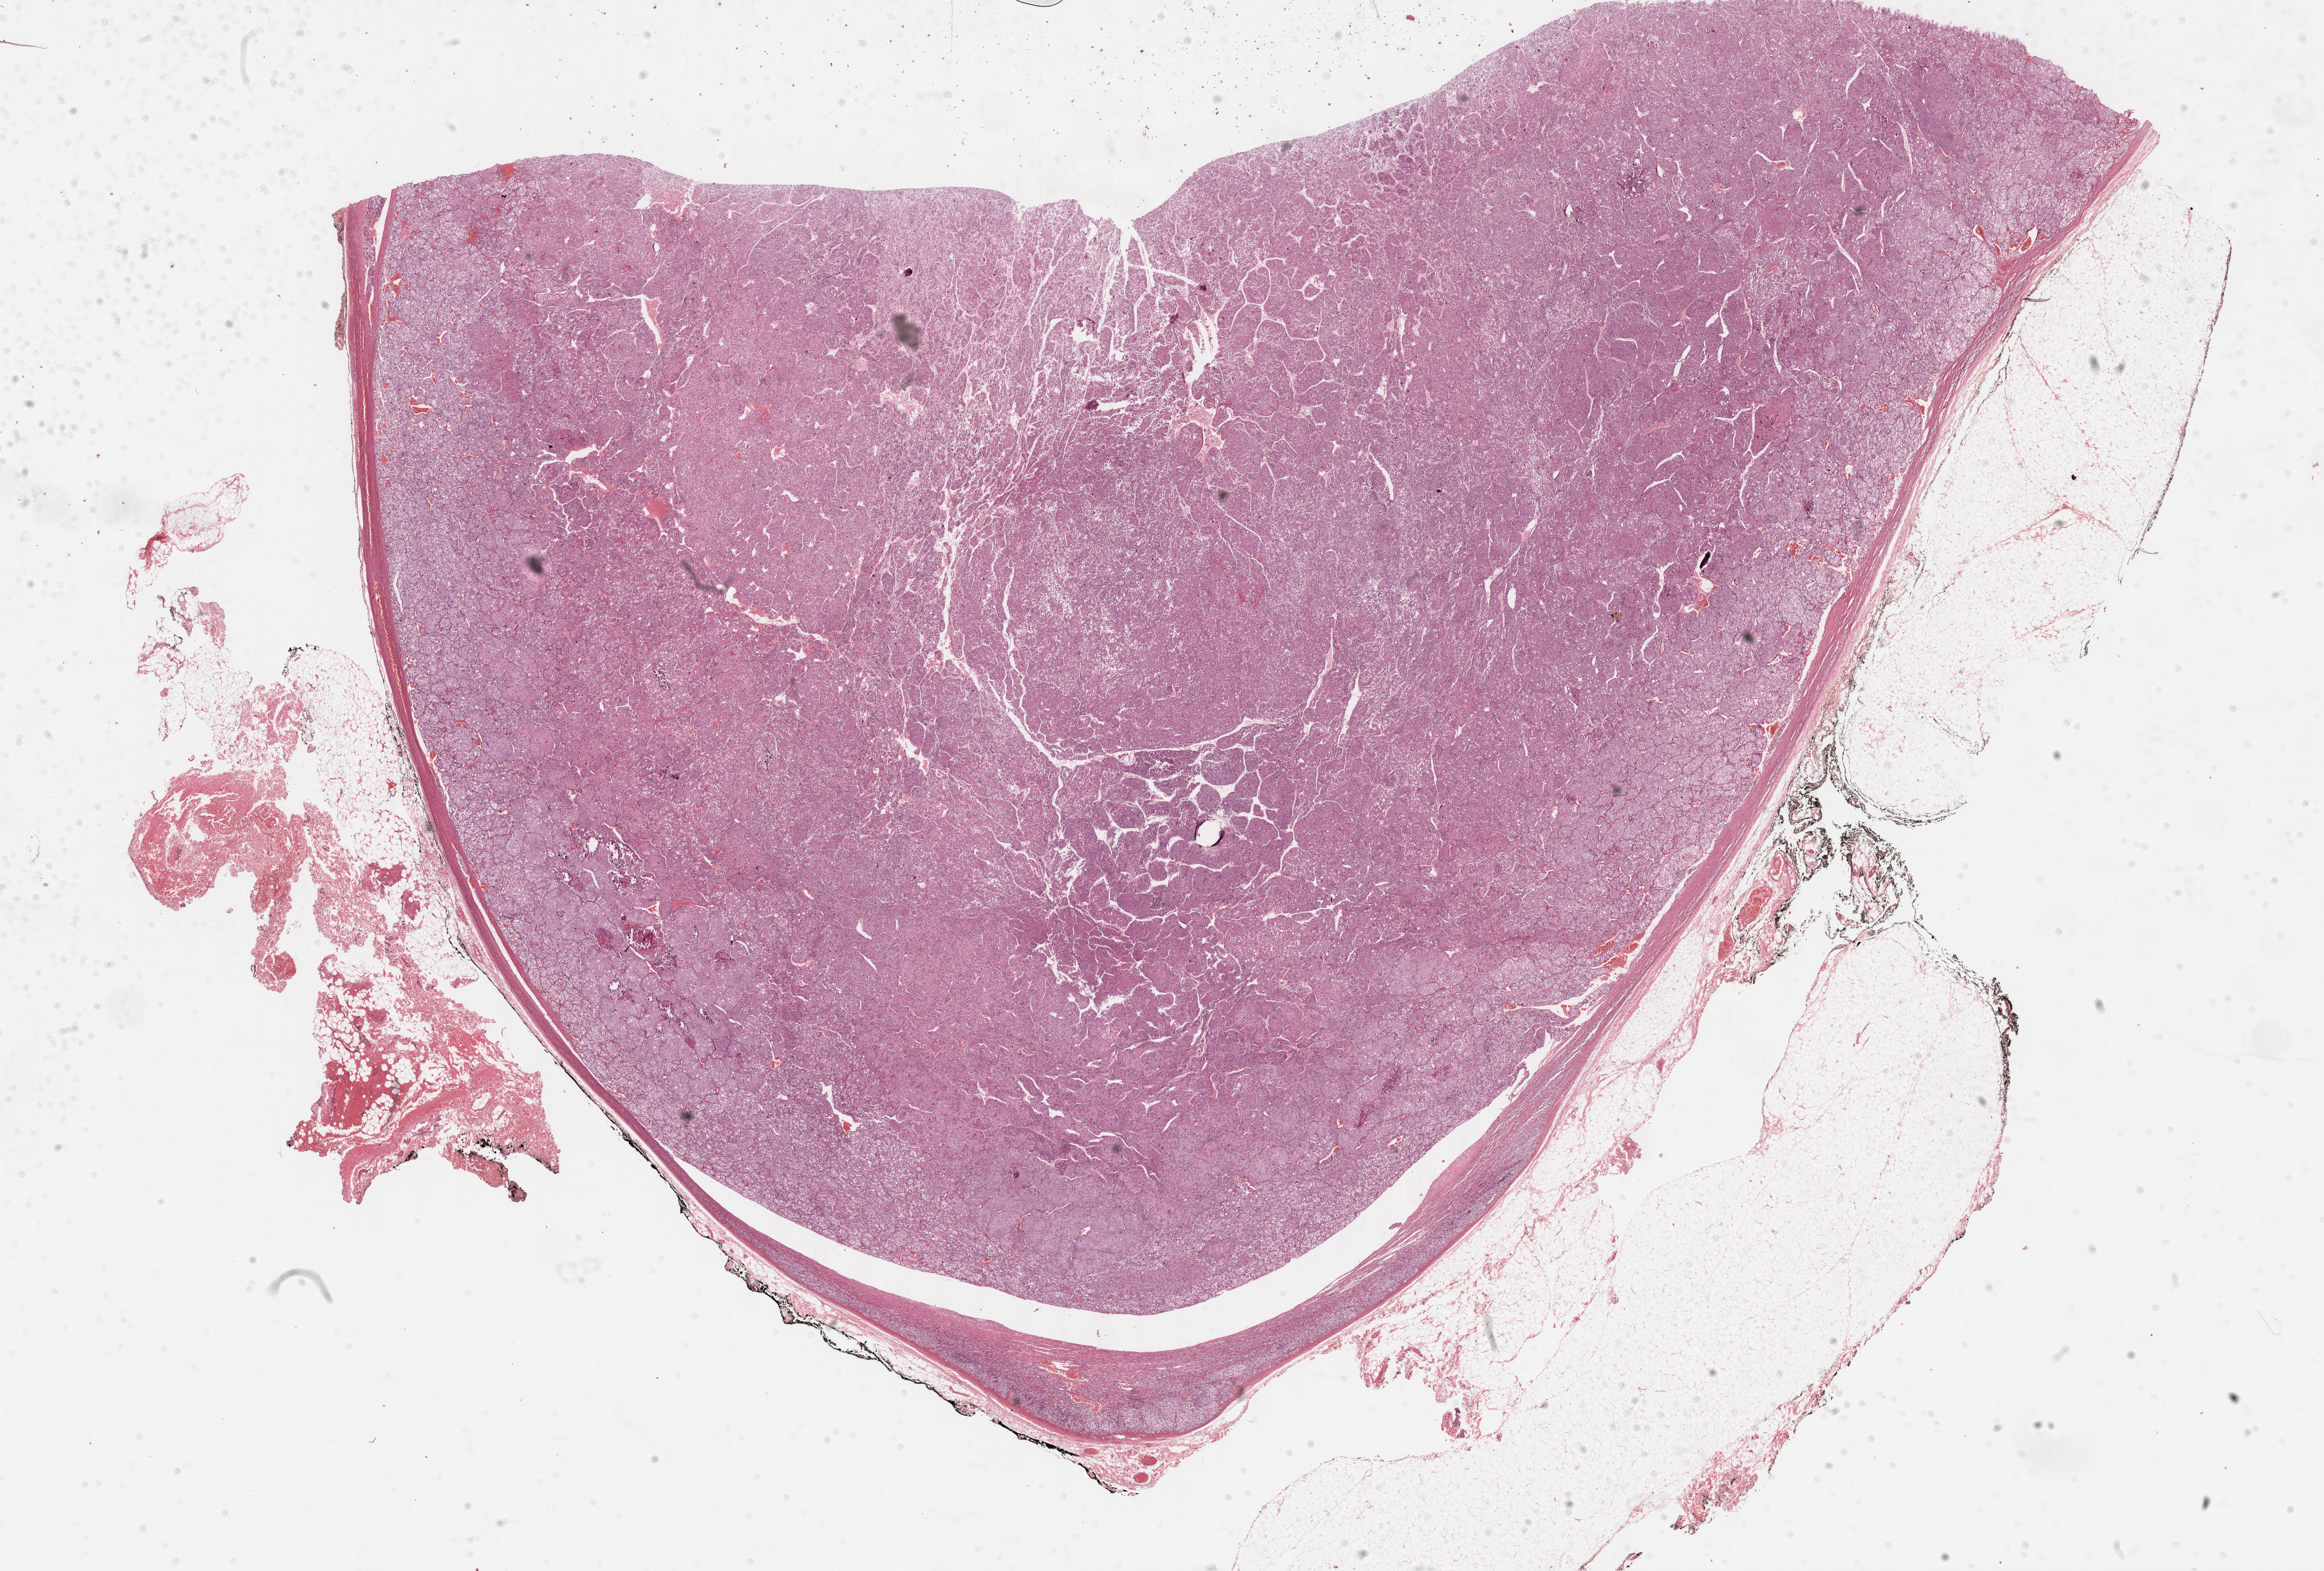
Hematoxylin and eosin (H&E) stained whole-slide image — low-resolution overview of the scanned area, about 29.2 x 19.7 mm (slide scanned at 40x); FFPE section; primary tumour sample from the adrenal cortex. Female, age 23 years at initial diagnosis.
Histologic diagnosis: Adrenal cortical carcinoma (cortex of adrenal gland). Laterality: left. Lymph nodes positive (case pathology): 0 of 4 examined.